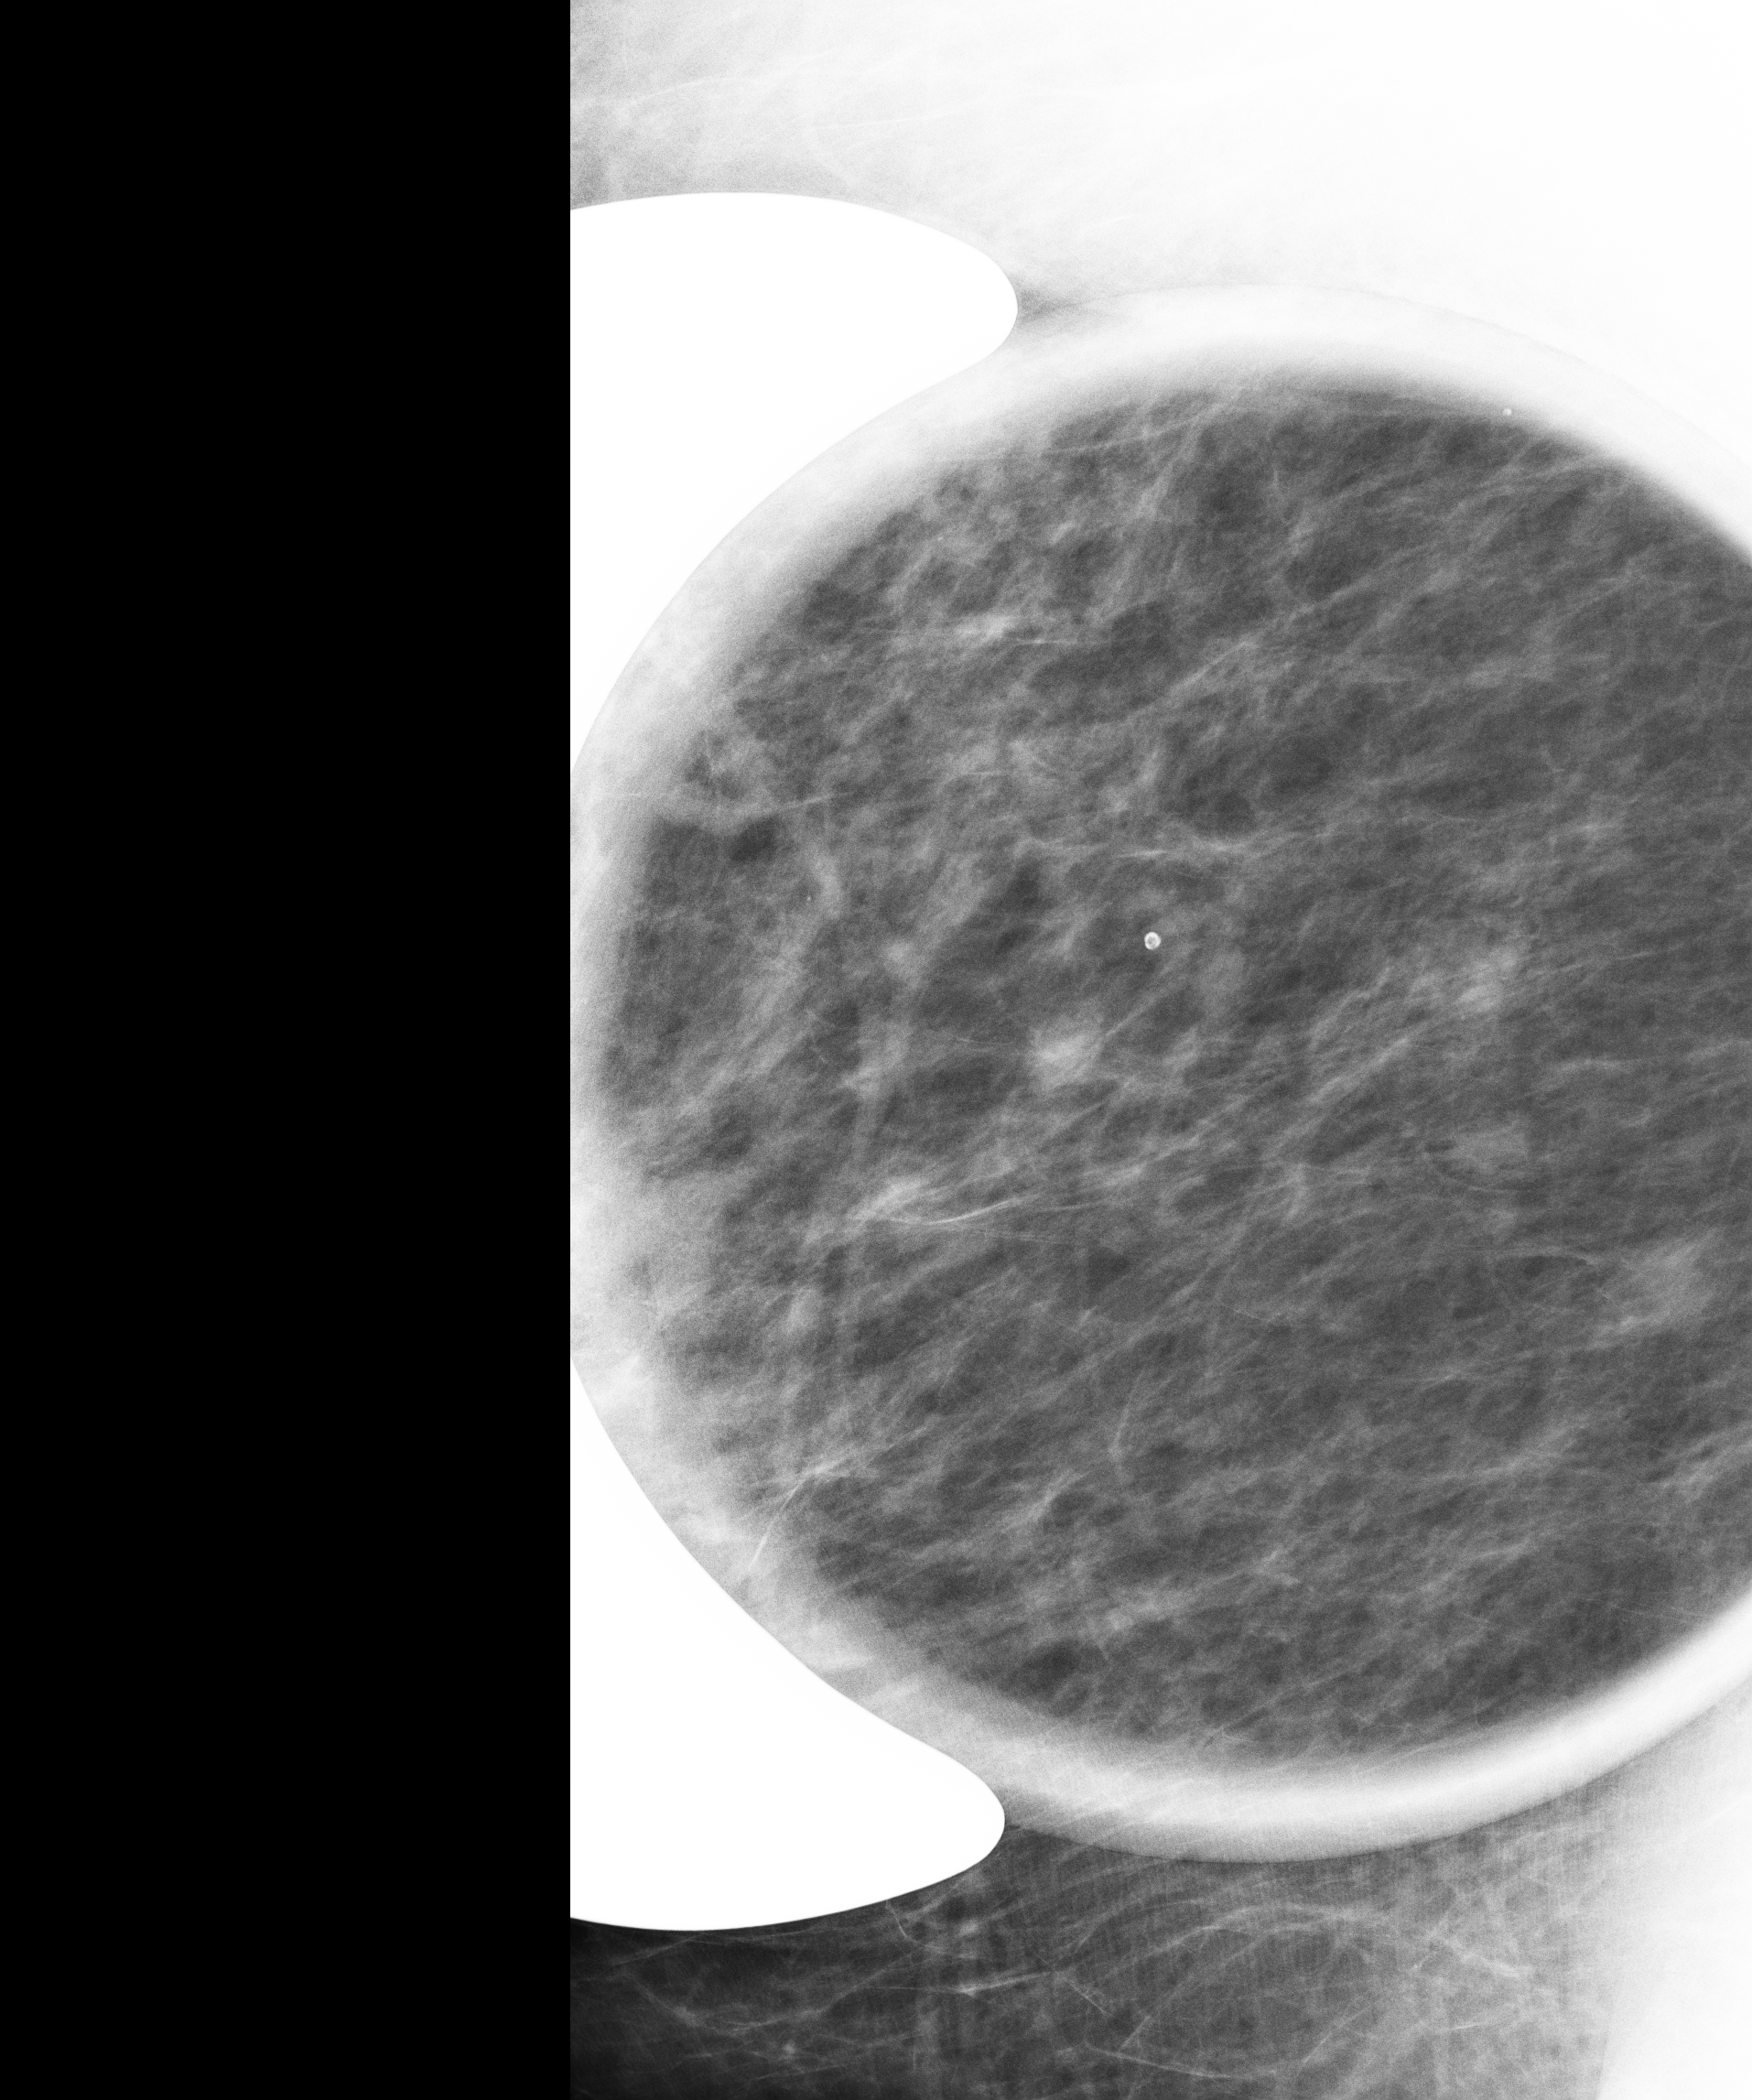
Digital mammogram (FFDM); left breast; lateromedial (LM) view; diagnostic examination (additional views); compressed breast thickness 74 mm. Patient: female, 53 years.
- BI-RADS breast density category at the screening exam (both breasts, scale 1–4): 3
- final BI-RADS assessment for this screening round (tomosynthesis exam, both breasts): category 4
- recall: recalled for additional imaging after this screen